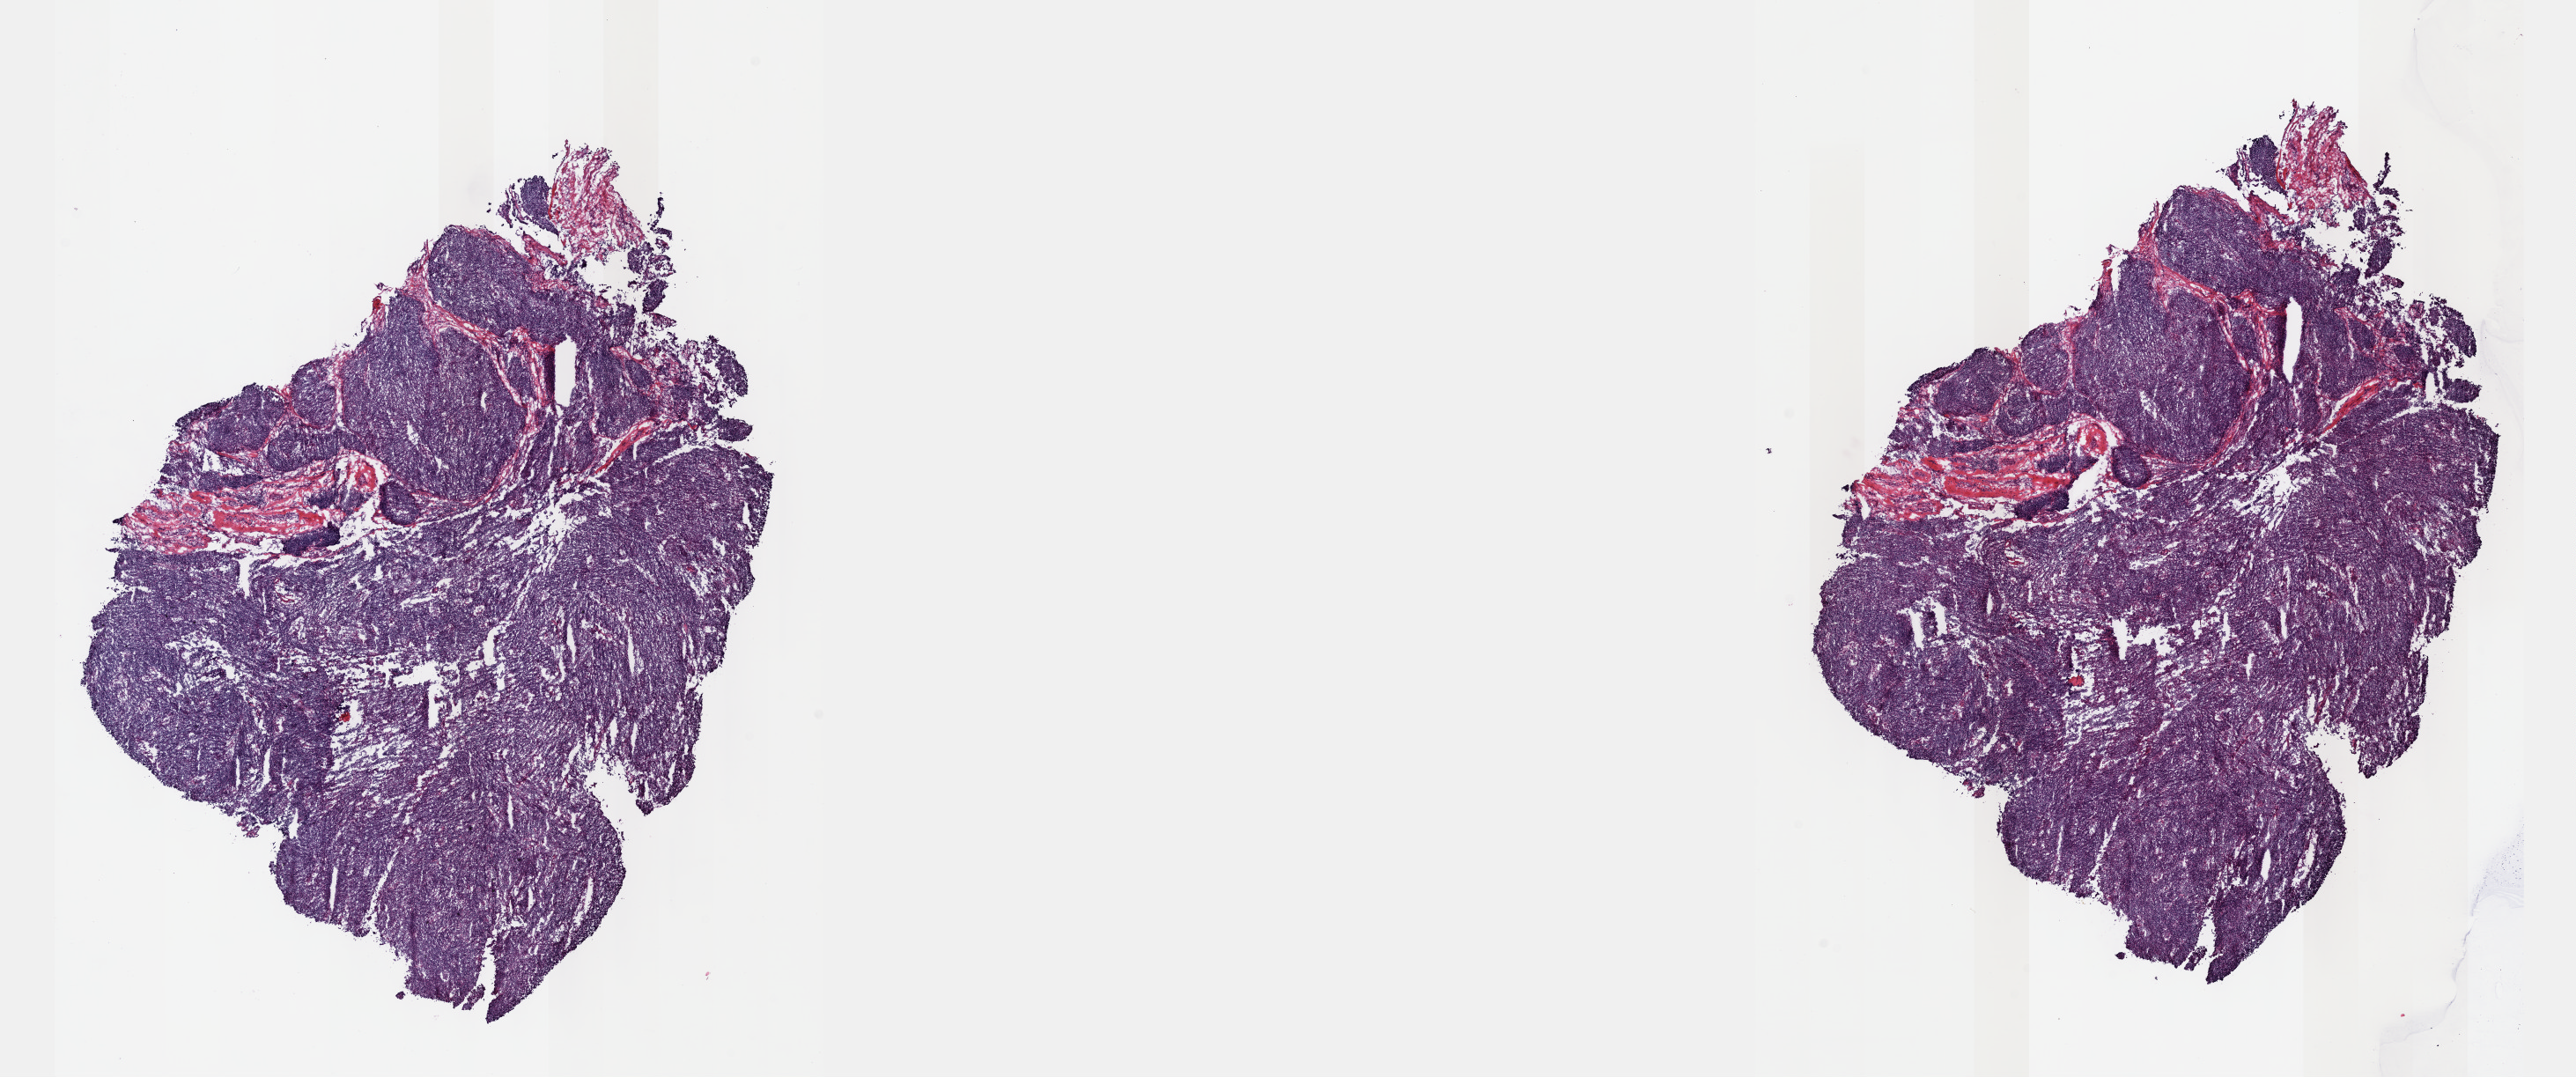
Digitized Hematoxylin and eosin (H&E) stained tissue section (whole slide), low-resolution overview of the scanned area, about 23.6 x 9.9 mm. Frozen section. Sample: primary tumour, thymus. Male patient; age at initial diagnosis 45 years. Pathologist review of this section (percent, as recorded): tumour cells 100%, tumour nuclei 80%, normal cells 0%, stromal cells 0%, necrosis 0%. Infiltration values recorded for this section: lymphocyte infiltration 2%, monocyte infiltration 0%, neutrophil infiltration 0%.
- pathologic diagnosis: Thymoma, type B1, malignant